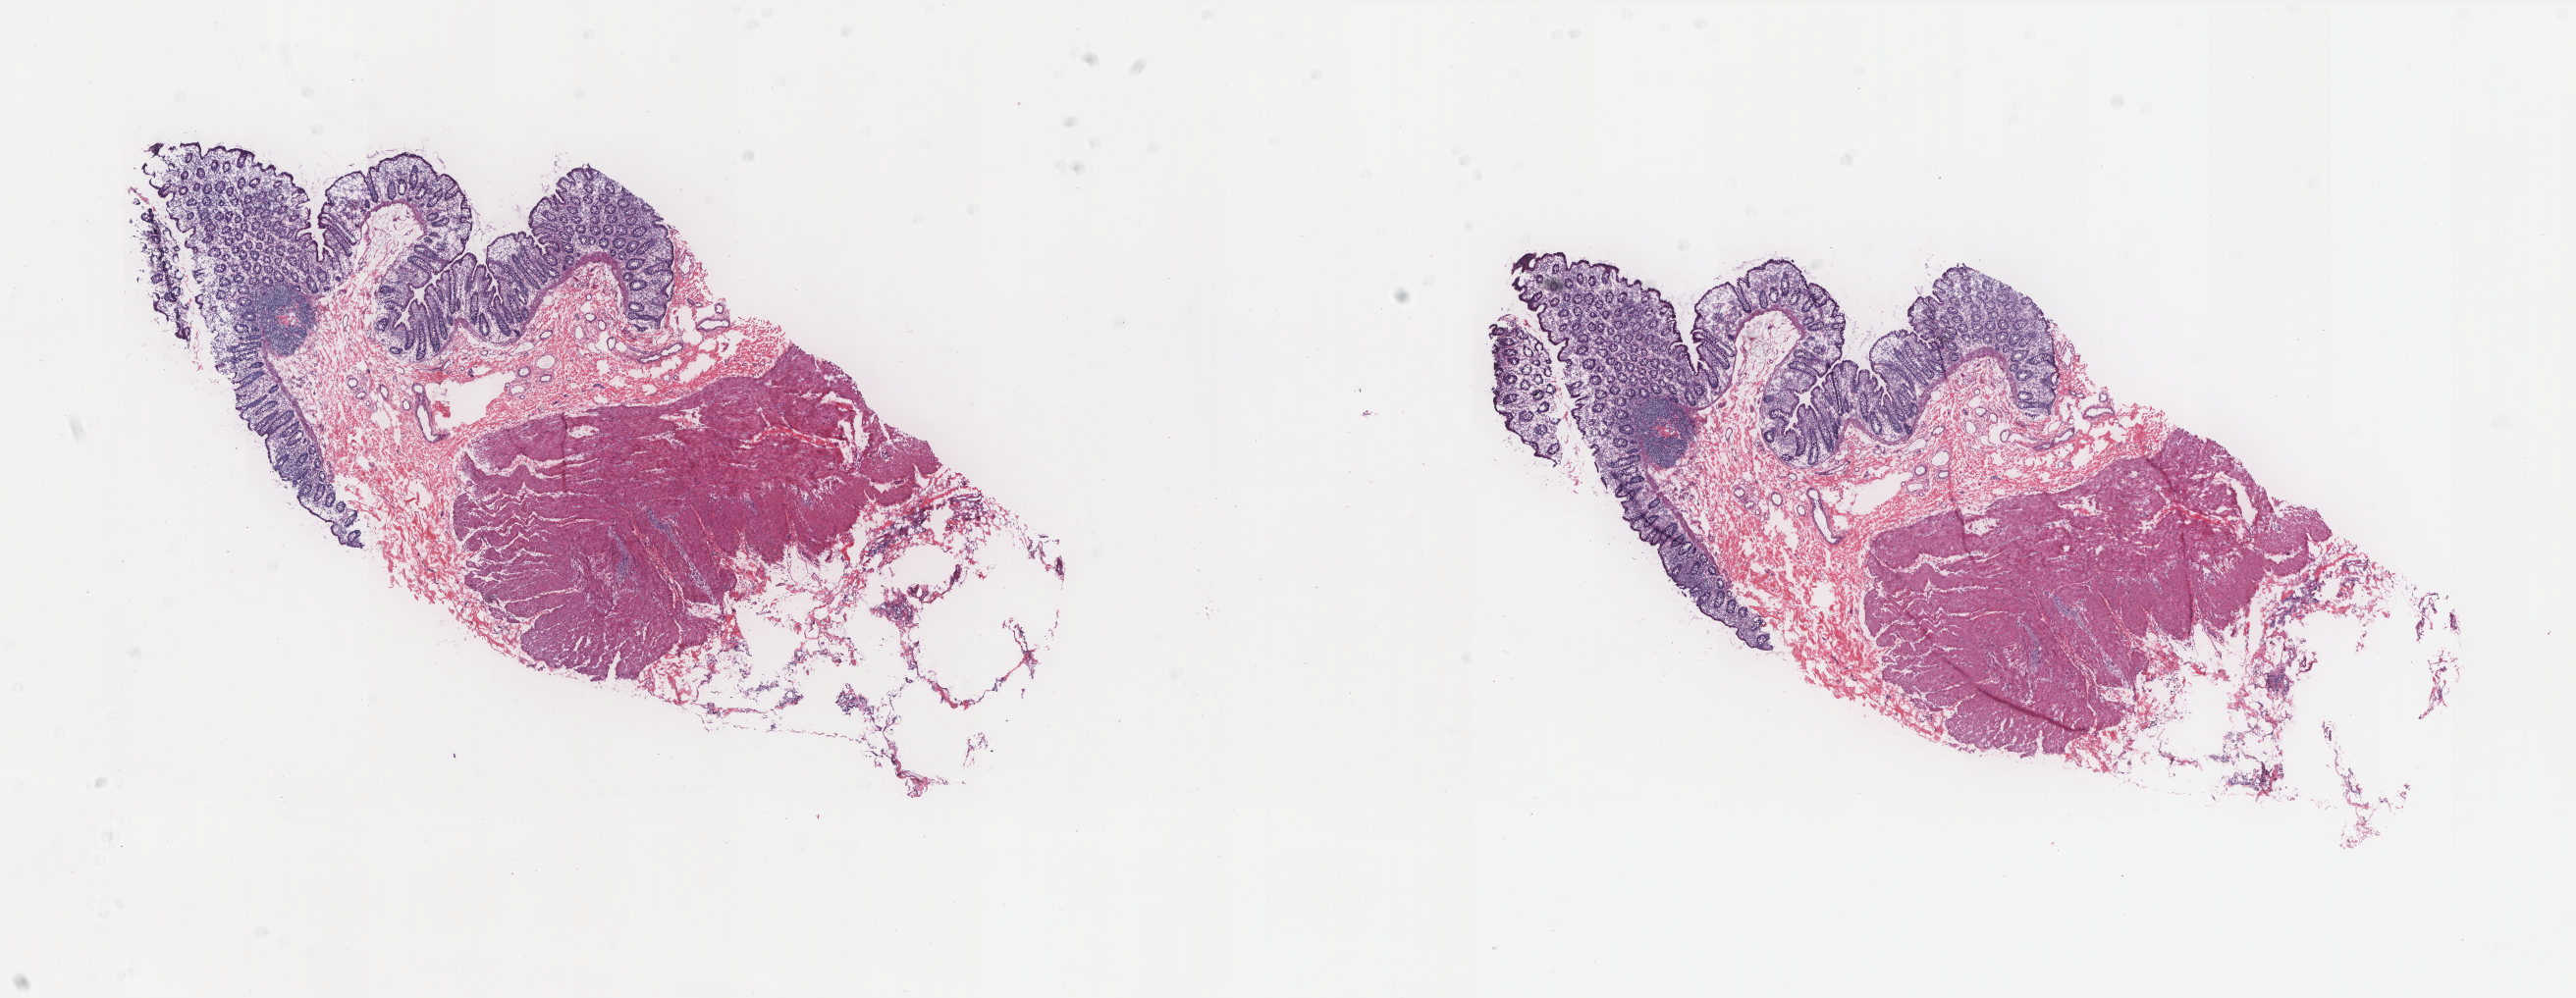
Digitized Hematoxylin and eosin (H&E) stained tissue section (whole slide), a low-resolution overview of the entire scanned area, about 21.0 x 8.1 mm; frozen section; colon, solid tissue normal (non-tumour tissue) sample. Male patient; age at initial diagnosis 68 years. Composition of this section per pathologist review: tumour cells 0%, normal cells 100%. Inflammatory infiltration, as recorded: lymphocyte infiltration 45%, monocyte infiltration 10%, neutrophil infiltration 0%.
• this section: solid tissue normal (non-tumour) sample from the same patient
• patient diagnosis: Adenocarcinoma, NOS (ascending colon)